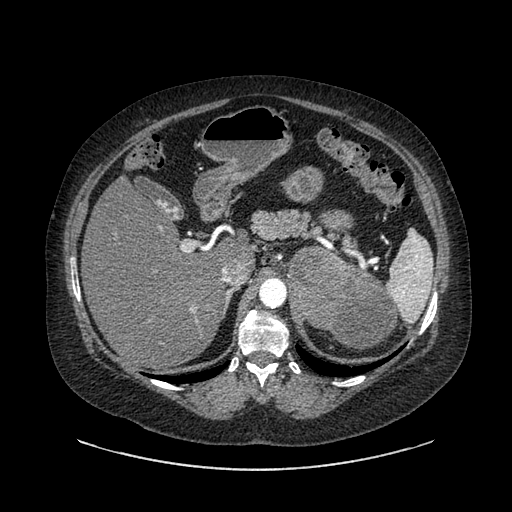
Contrast-enhanced abdominal CT, one axial slice; 120 kVp; intravenous contrast given; soft-tissue window (W 400 / L 40 HU); 0.62 mm slice thickness; 512 × 512 image matrix, field of view 460 × 460 mm. Female patient, age 61 years. Case-level facts recorded for this patient, not image findings: diagnosis: adrenocortical carcinoma; tumour side: left adrenal; tumour size at pathology: 13 cm; Ki-67 index: 79 %; stage (as recorded): 2.
Annotated regions visible in this slice (semi-automatically segmented with operator editing):
- mass: box from (x=288, y=249) to (x=393, y=349) px